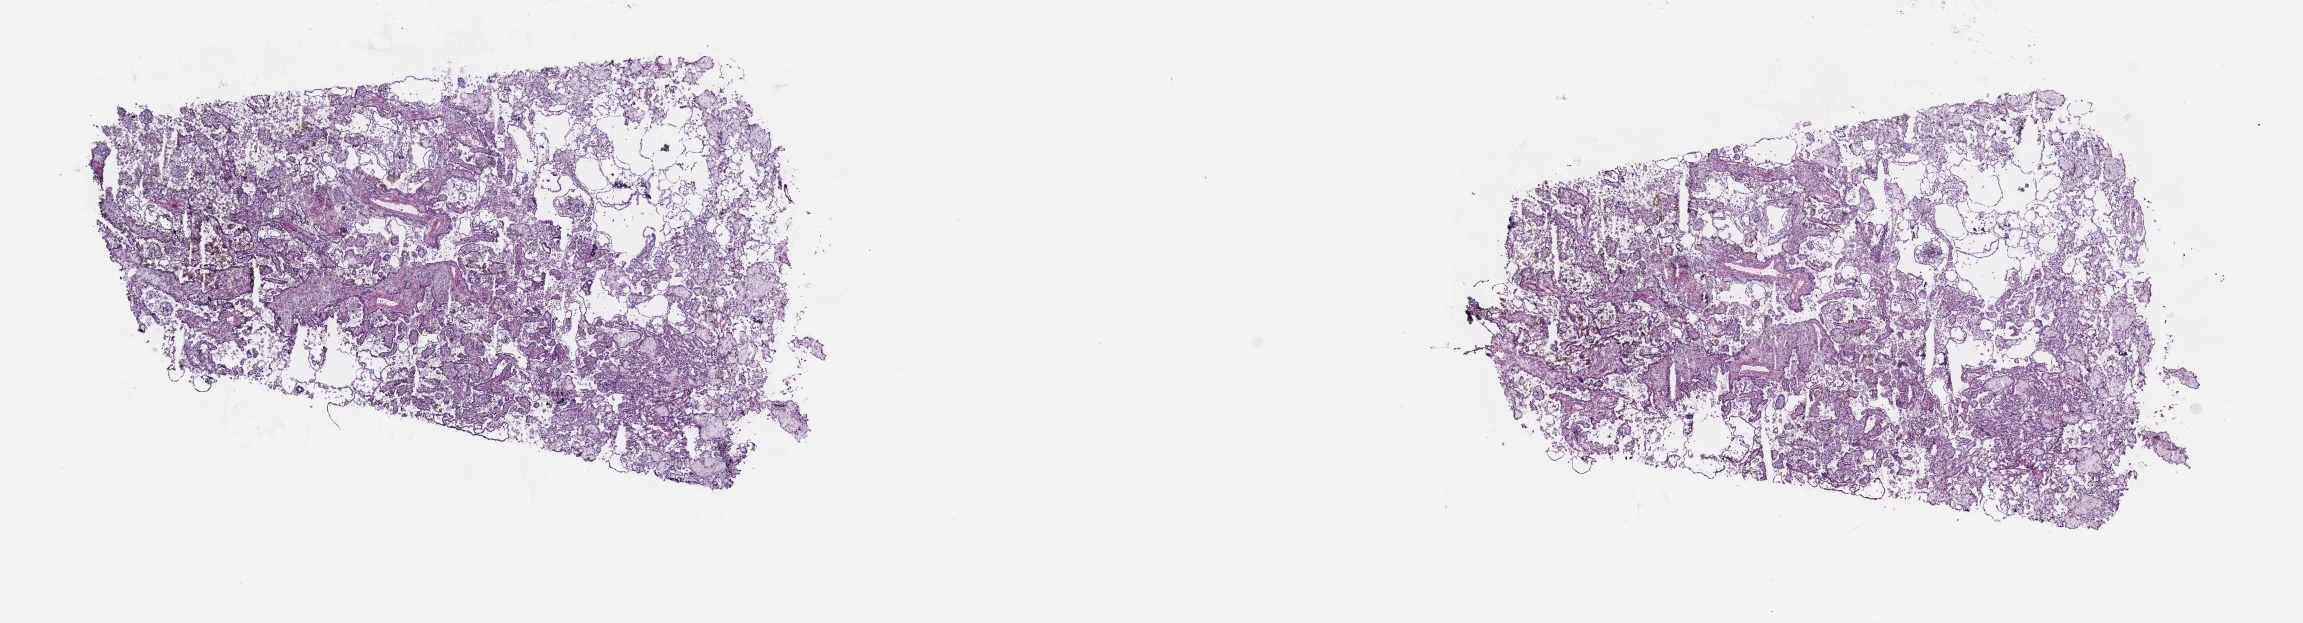
Whole-slide histology image, Hematoxylin and eosin (H&E) stained, a low-resolution overview of the entire scanned area, about 18.6 x 5.0 mm, frozen section, sample: primary tumour, kidney. Male patient; age at initial diagnosis 69 years. Slide review estimates, as recorded: tumour cells 70%, tumour nuclei 70%, normal cells 0%, stromal cells 30%, necrosis 0%. Infiltration values recorded for this section: lymphocyte infiltration 2%, monocyte infiltration 7%, neutrophil infiltration 1%.
• AJCC pathologic stage: I (7th edition)
• laterality: left
• diagnosis: Papillary adenocarcinoma, NOS